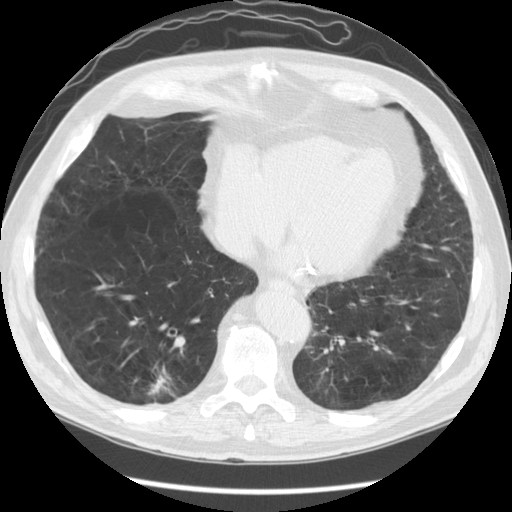
Low-dose screening chest CT, one axial slice. Slice 46 of 141 in the series (ordered by position). Reconstruction kernel STANDARD. 120 kVp. Lung window (W 1500 / L -600 HU). 2.5 mm slice thickness. 512 × 512 image matrix.
Outlined on this slice (manually delineated by an expert):
- lesion 1 (tumor, lower lobe of right lung): bounding box <148,368,174,396> (left, top, right, bottom; pixels)